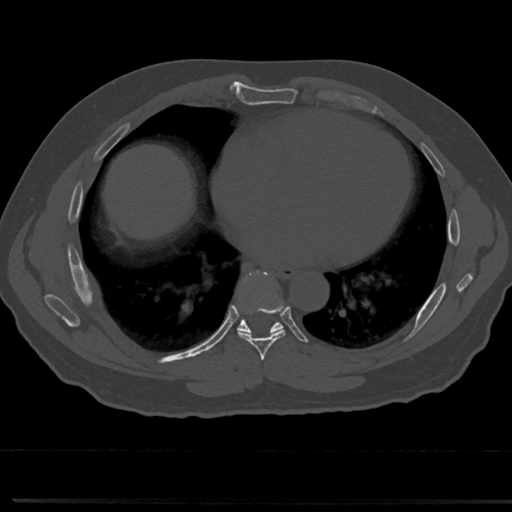
CT including the spine, one axial slice; slice 386 of 817 in the series (ordered by position); reconstruction kernel Br40s/3; bone window (W 1800 / L 400 HU); 0.5 mm slice thickness; 512 × 512 image matrix, field of view 355 × 355 mm. Male patient, age 61 years. Case-level facts recorded for this patient, not image findings: primary cancer: prostate.
Outlined on this slice (semi-automatic segmentation, software-assisted and operator-edited):
- T6 vertebra: bounding box <260,366,268,377> (left, top, right, bottom; pixels)
- T7 vertebra: <226,274,309,354>